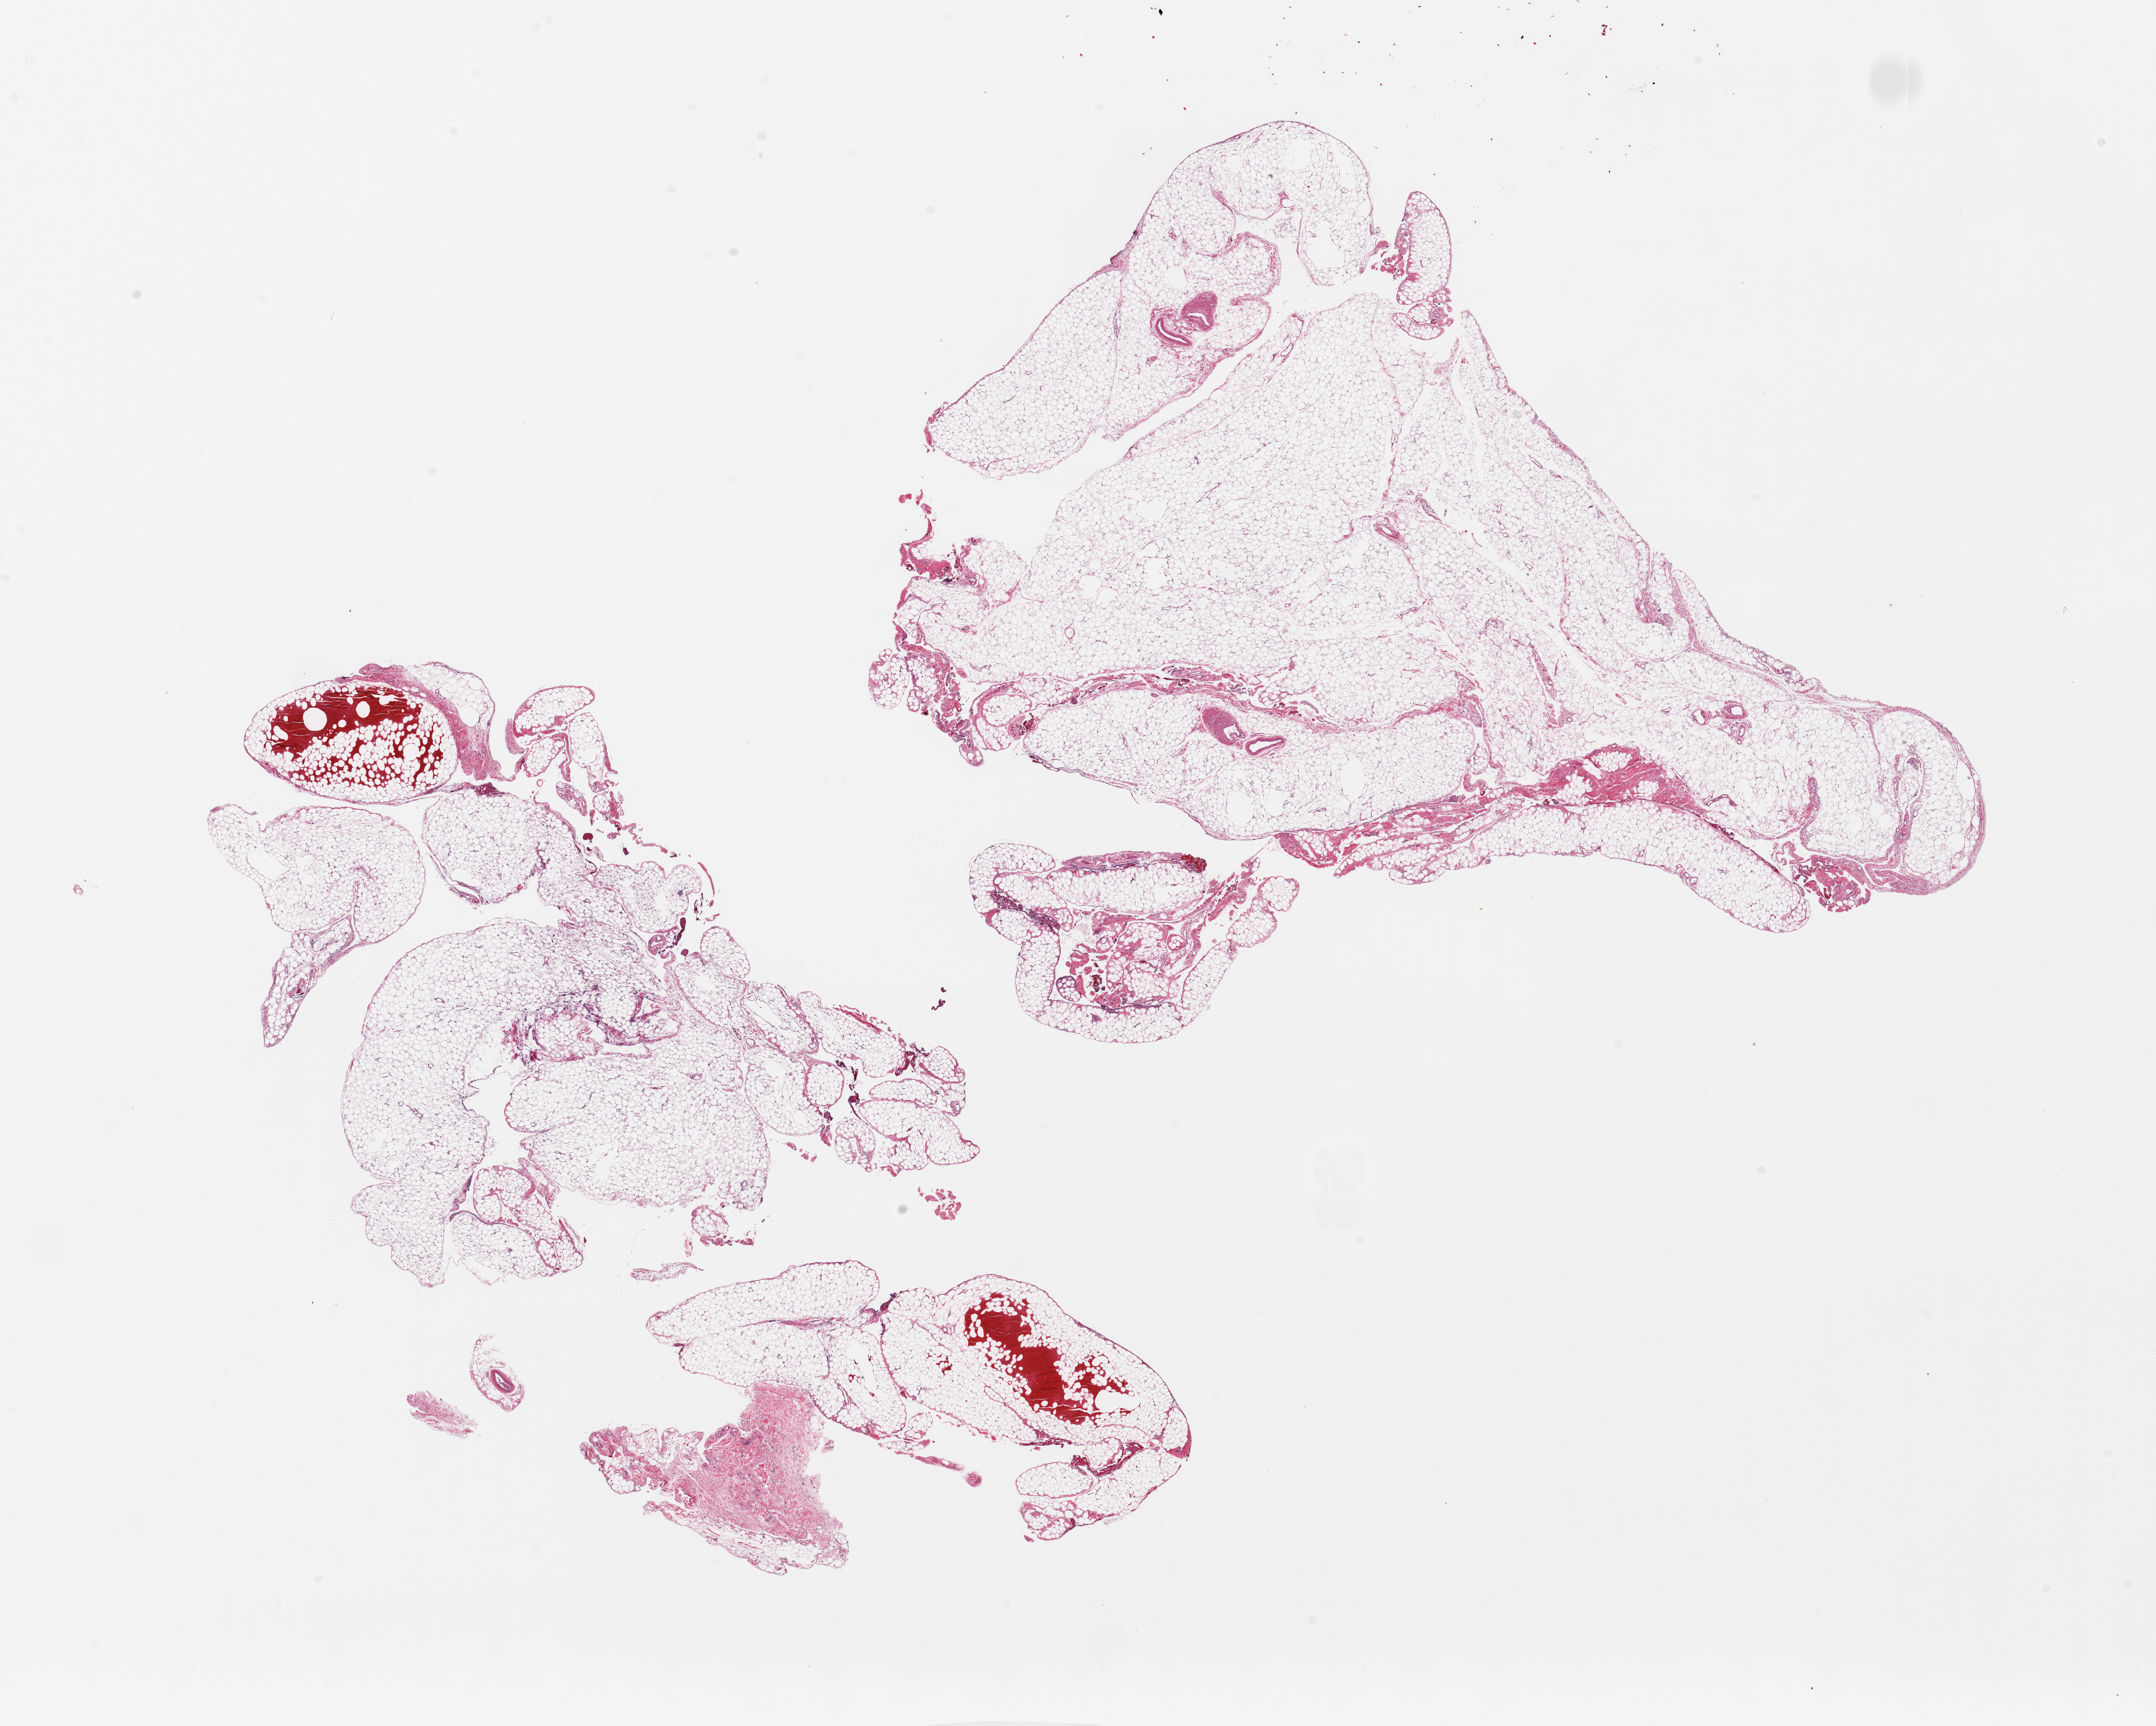
Digitized hematoxylin and eosin (H&E)-stained section — whole scanned area (about 25.6 x 20.5 mm, slide scanned at 20x) shown as a low-resolution overview, PAXgene-fixed, paraffin-embedded tissue, section of omentum (target tissue), tissue donor sample. Donor: female.
Reviewer comment on this tissue sample: 2 pieces, 14x7 & 13.5x11mm.